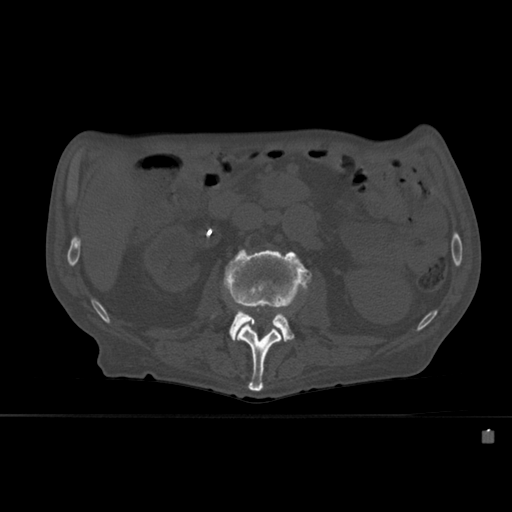
CT including the spine, one axial slice; position 224 of 527 along the scan axis; bone window (W 1800 / L 400 HU); 1.5 mm slice thickness; 512 × 512 image matrix. Male patient, age 78 years. Case-level facts recorded for this patient, not image findings: primary cancer: prostate.
Structures marked on this image (semi-automatic segmentation, software-assisted and operator-edited):
- L2 vertebra: bounding box [x1, y1, x2, y2] px = [225, 290, 282, 392]
- L3 vertebra: [223, 248, 312, 341]